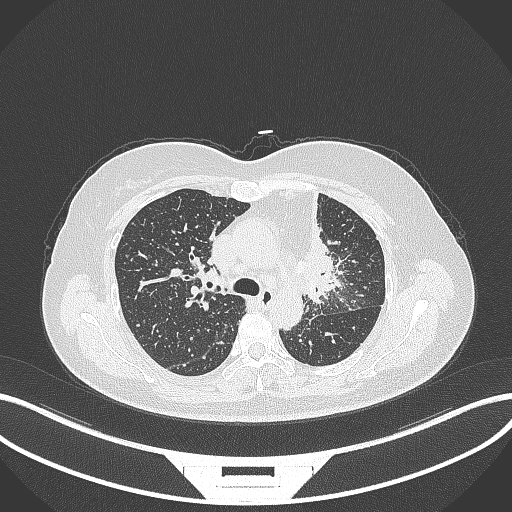
Chest CT, one axial slice. Slice 225 of 348 in the series (ordered by position). Reconstruction kernel B70f. Lung window (W 1500 / L -600 HU). 1 mm slice thickness. 512 × 512 image matrix, field of view 400 × 400 mm. Female patient, age 49 years. From the clinical record (not read from this slice): clinical TNM (as recorded): T1c N0 M1.
Outlined on this slice (bounding box drawn by a radiologist):
- lung tumour (recorded histology: adenocarcinoma): box from (x=296, y=184) to (x=341, y=307) px